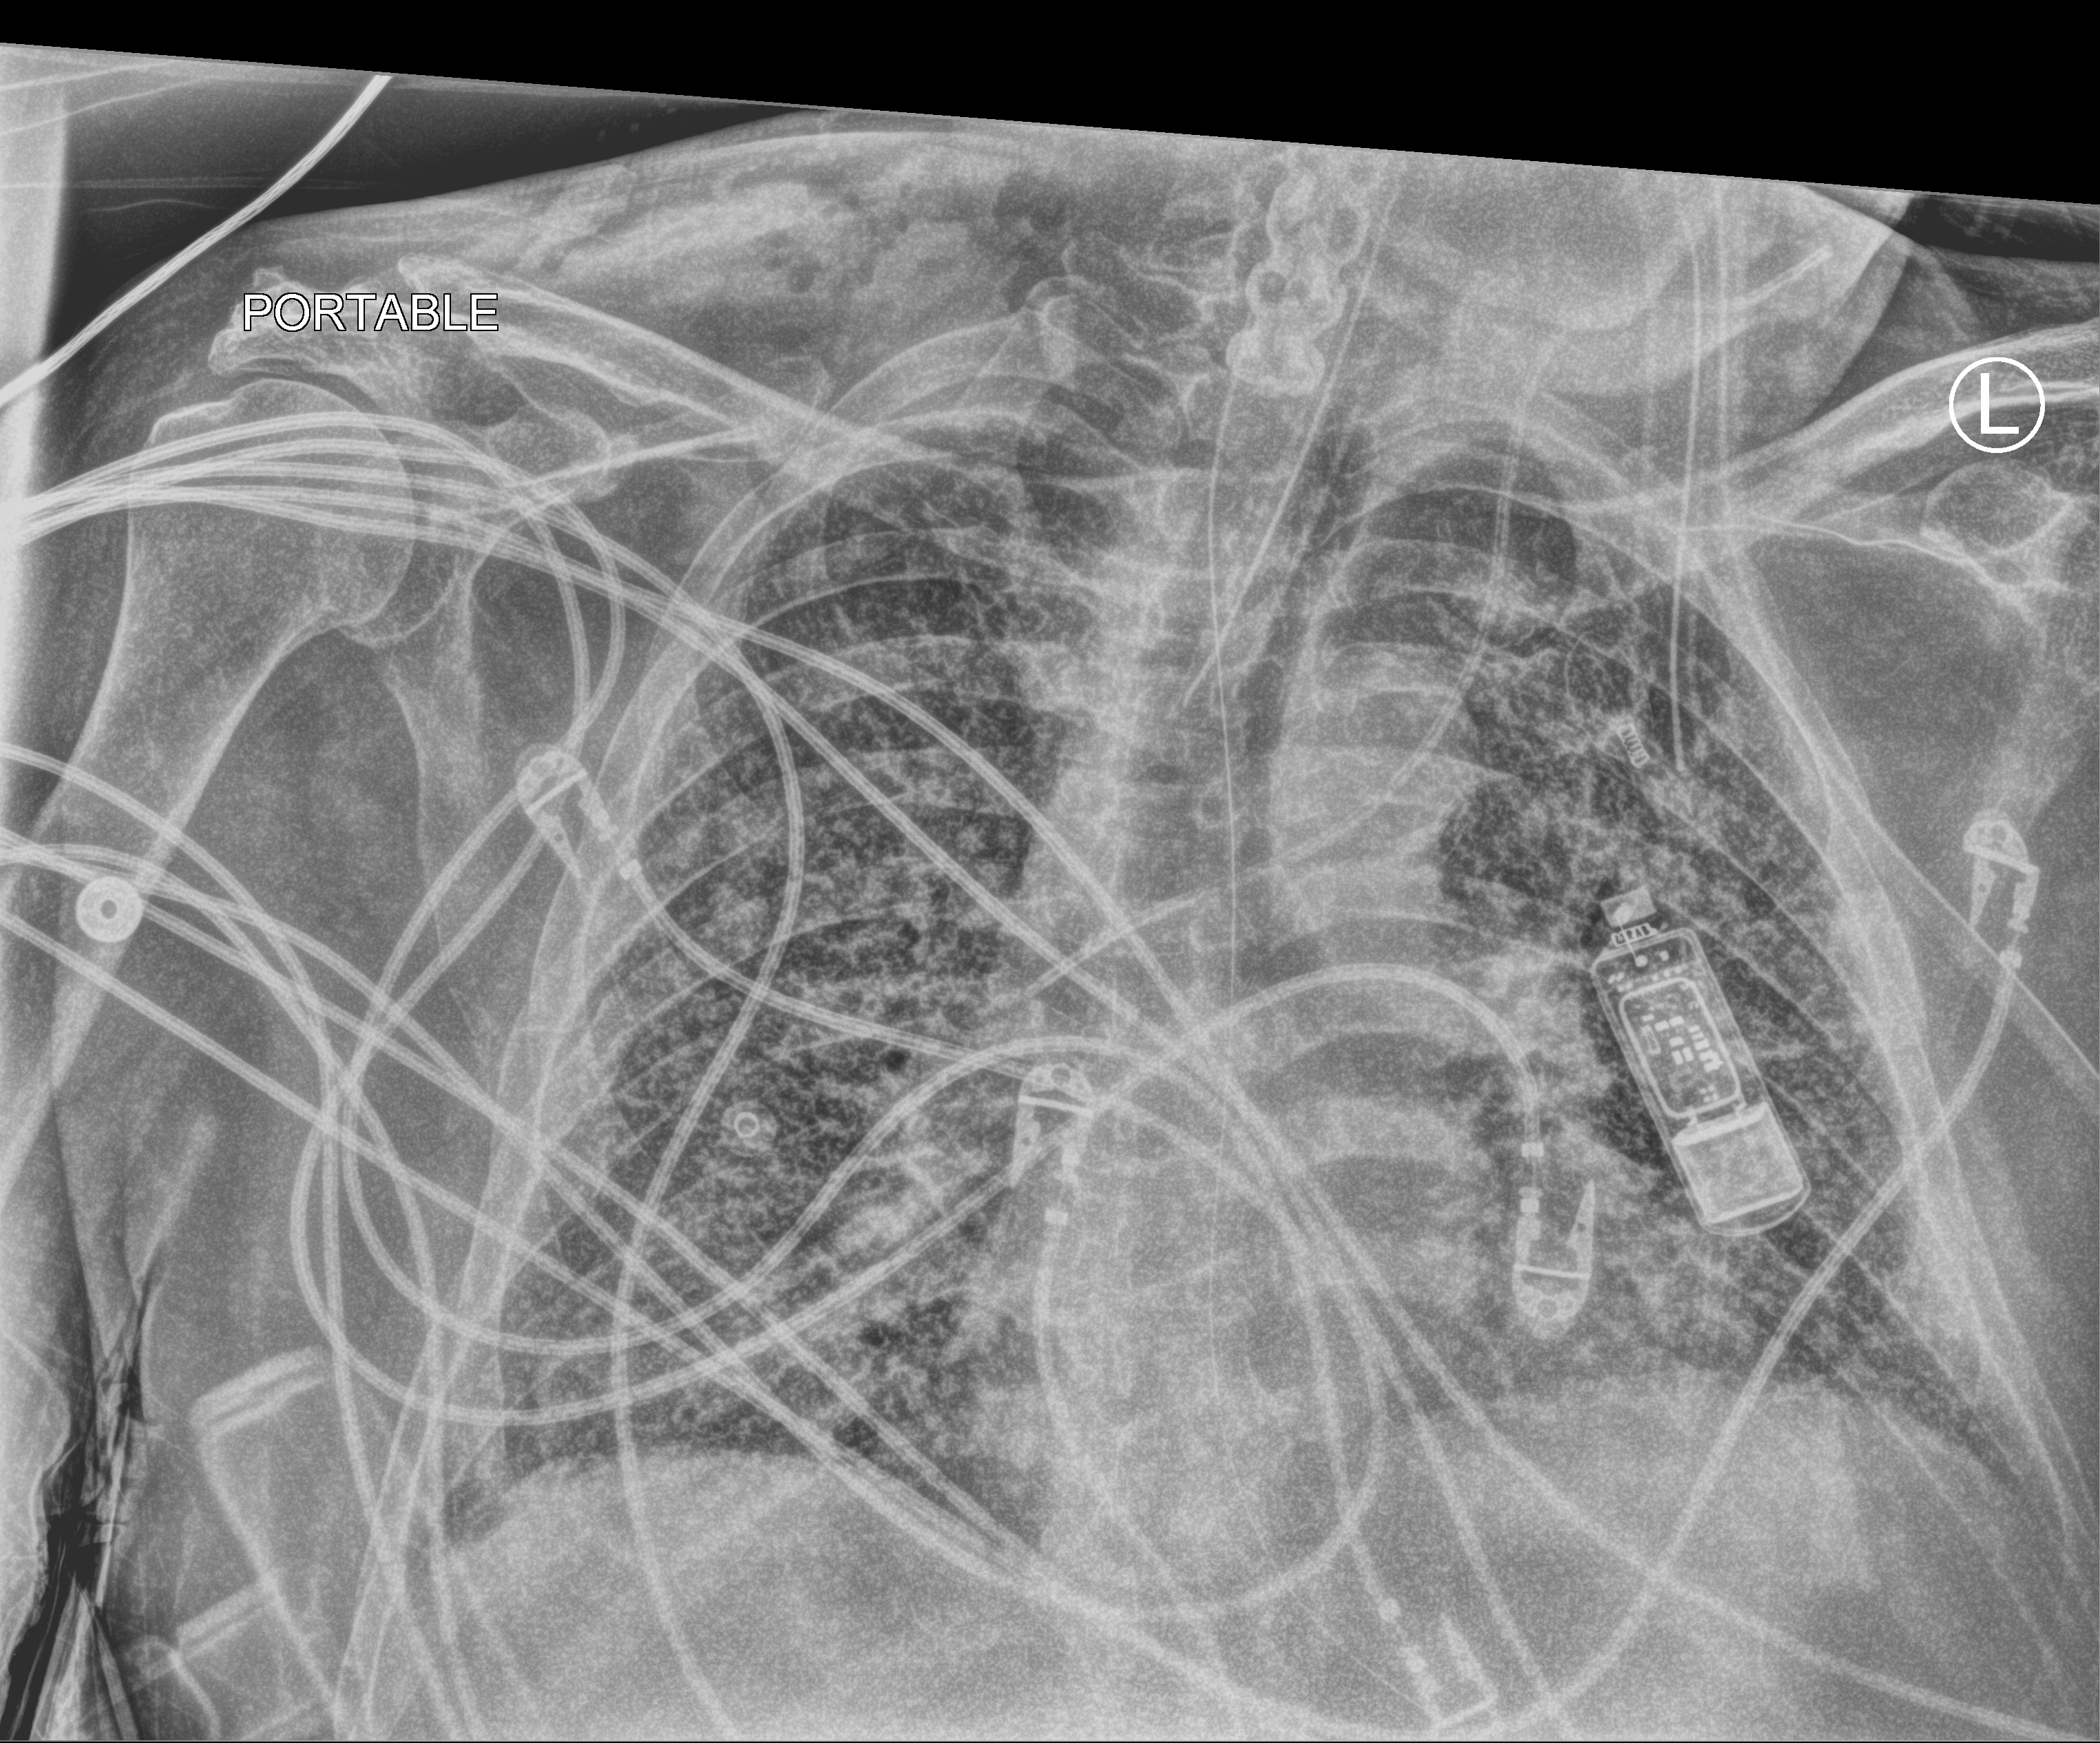
Bedside chest radiograph (computed radiography), anteroposterior (AP) projection. Patient hospitalised with COVID-19; male, aged 60–74 years.
Admission-level facts for this patient (not findings on this image; timing relative to this image not recorded):
- admitted to intensive care during this hospital stay: yes